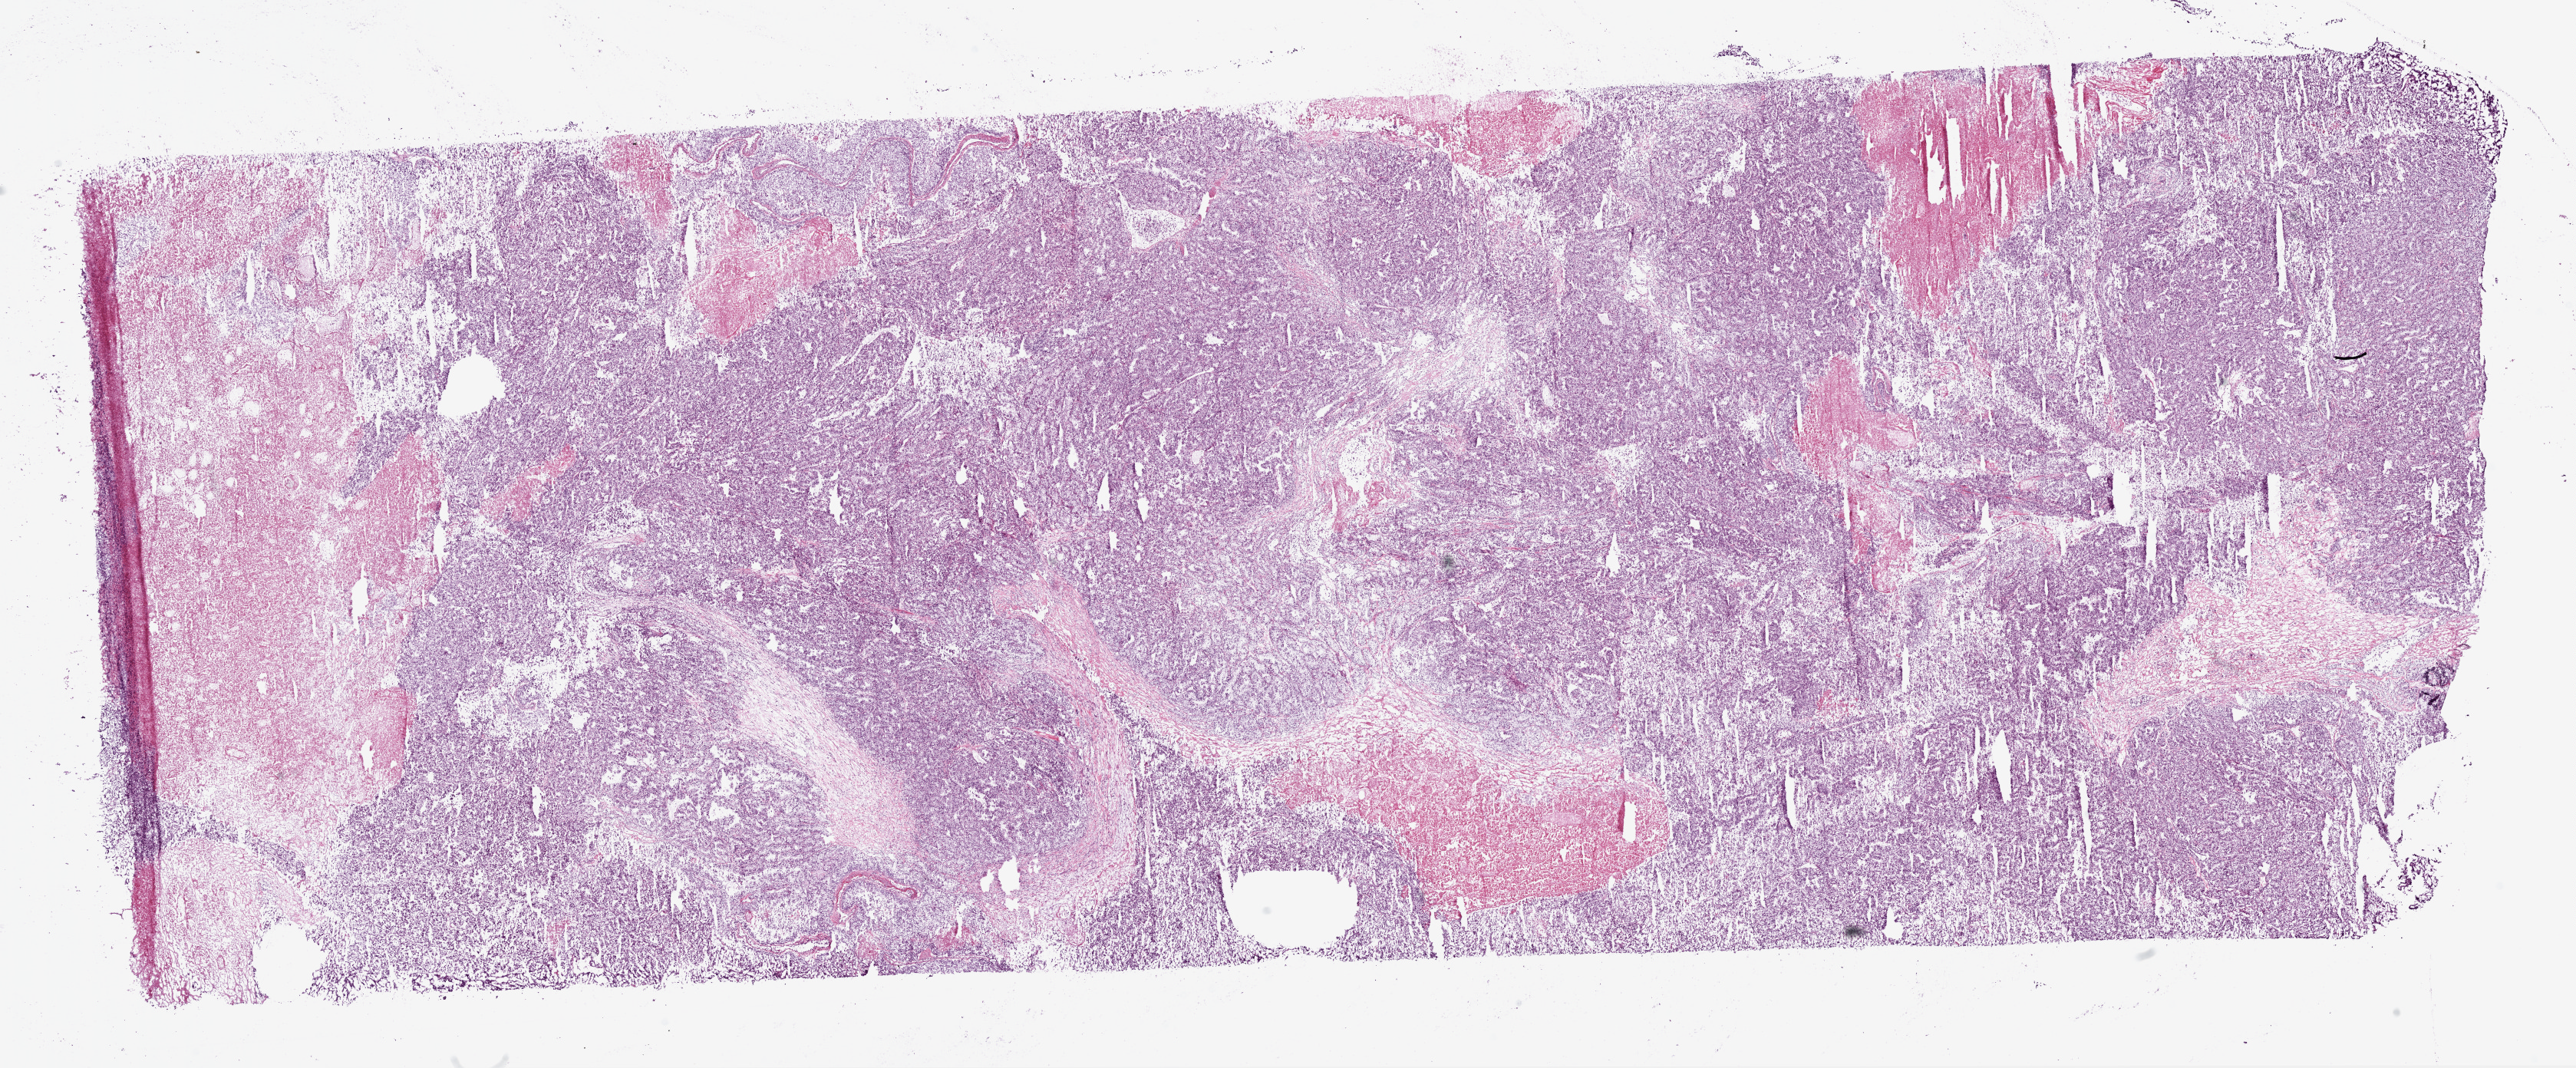
Digitized H&E-stained tissue section (whole slide), whole scanned area (about 27.1 x 11.2 mm, acquisition: 20x scan) shown as a low-resolution overview, frozen section from the bottom of the tissue portion, primary tumour sample from the kidney. Female patient; age at initial diagnosis 44 years. Histologic grade: G3 (poorly differentiated). Pathologist review of this section (percent, as recorded): tumour cells 90%, tumour nuclei 85%, normal cells 0%, stromal cells 10%, necrosis 15%.
Laterality: left. AJCC pathologic stage: IV. Diagnosis: Clear cell adenocarcinoma, NOS. TNM: T3a NX M1.